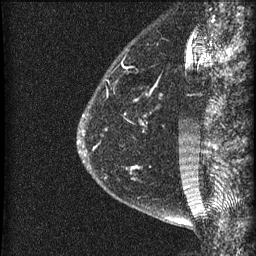
Breast MRI (dynamic contrast-enhanced), one sagittal slice. Slice 12 of 60 in the series (ordered by position). Dynamic contrast-enhanced series, image 2 of 3 at this slice position (ordered by acquisition). 1.5 T. TE 4.2 ms, TR 22.7 ms. 1.5 mm slice thickness. 256 × 256 image matrix. Patient: female, 48 years. Case-level facts recorded for this patient, not image findings: setting: breast cancer imaged before/during neoadjuvant chemotherapy; receptor status: triple-negative.
Annotated regions visible in this slice (semi-automatic segmentation, software-assisted and operator-edited):
- analysis volume of interest (the breast-tissue region the enhancement analysis was run in; not a lesion): box from (x=81, y=23) to (x=186, y=202) px
- tumour enhancement mask (voxels above the 90 % enhancement threshold inside the analysis volume of interest): (x=82, y=130)–(x=95, y=149)